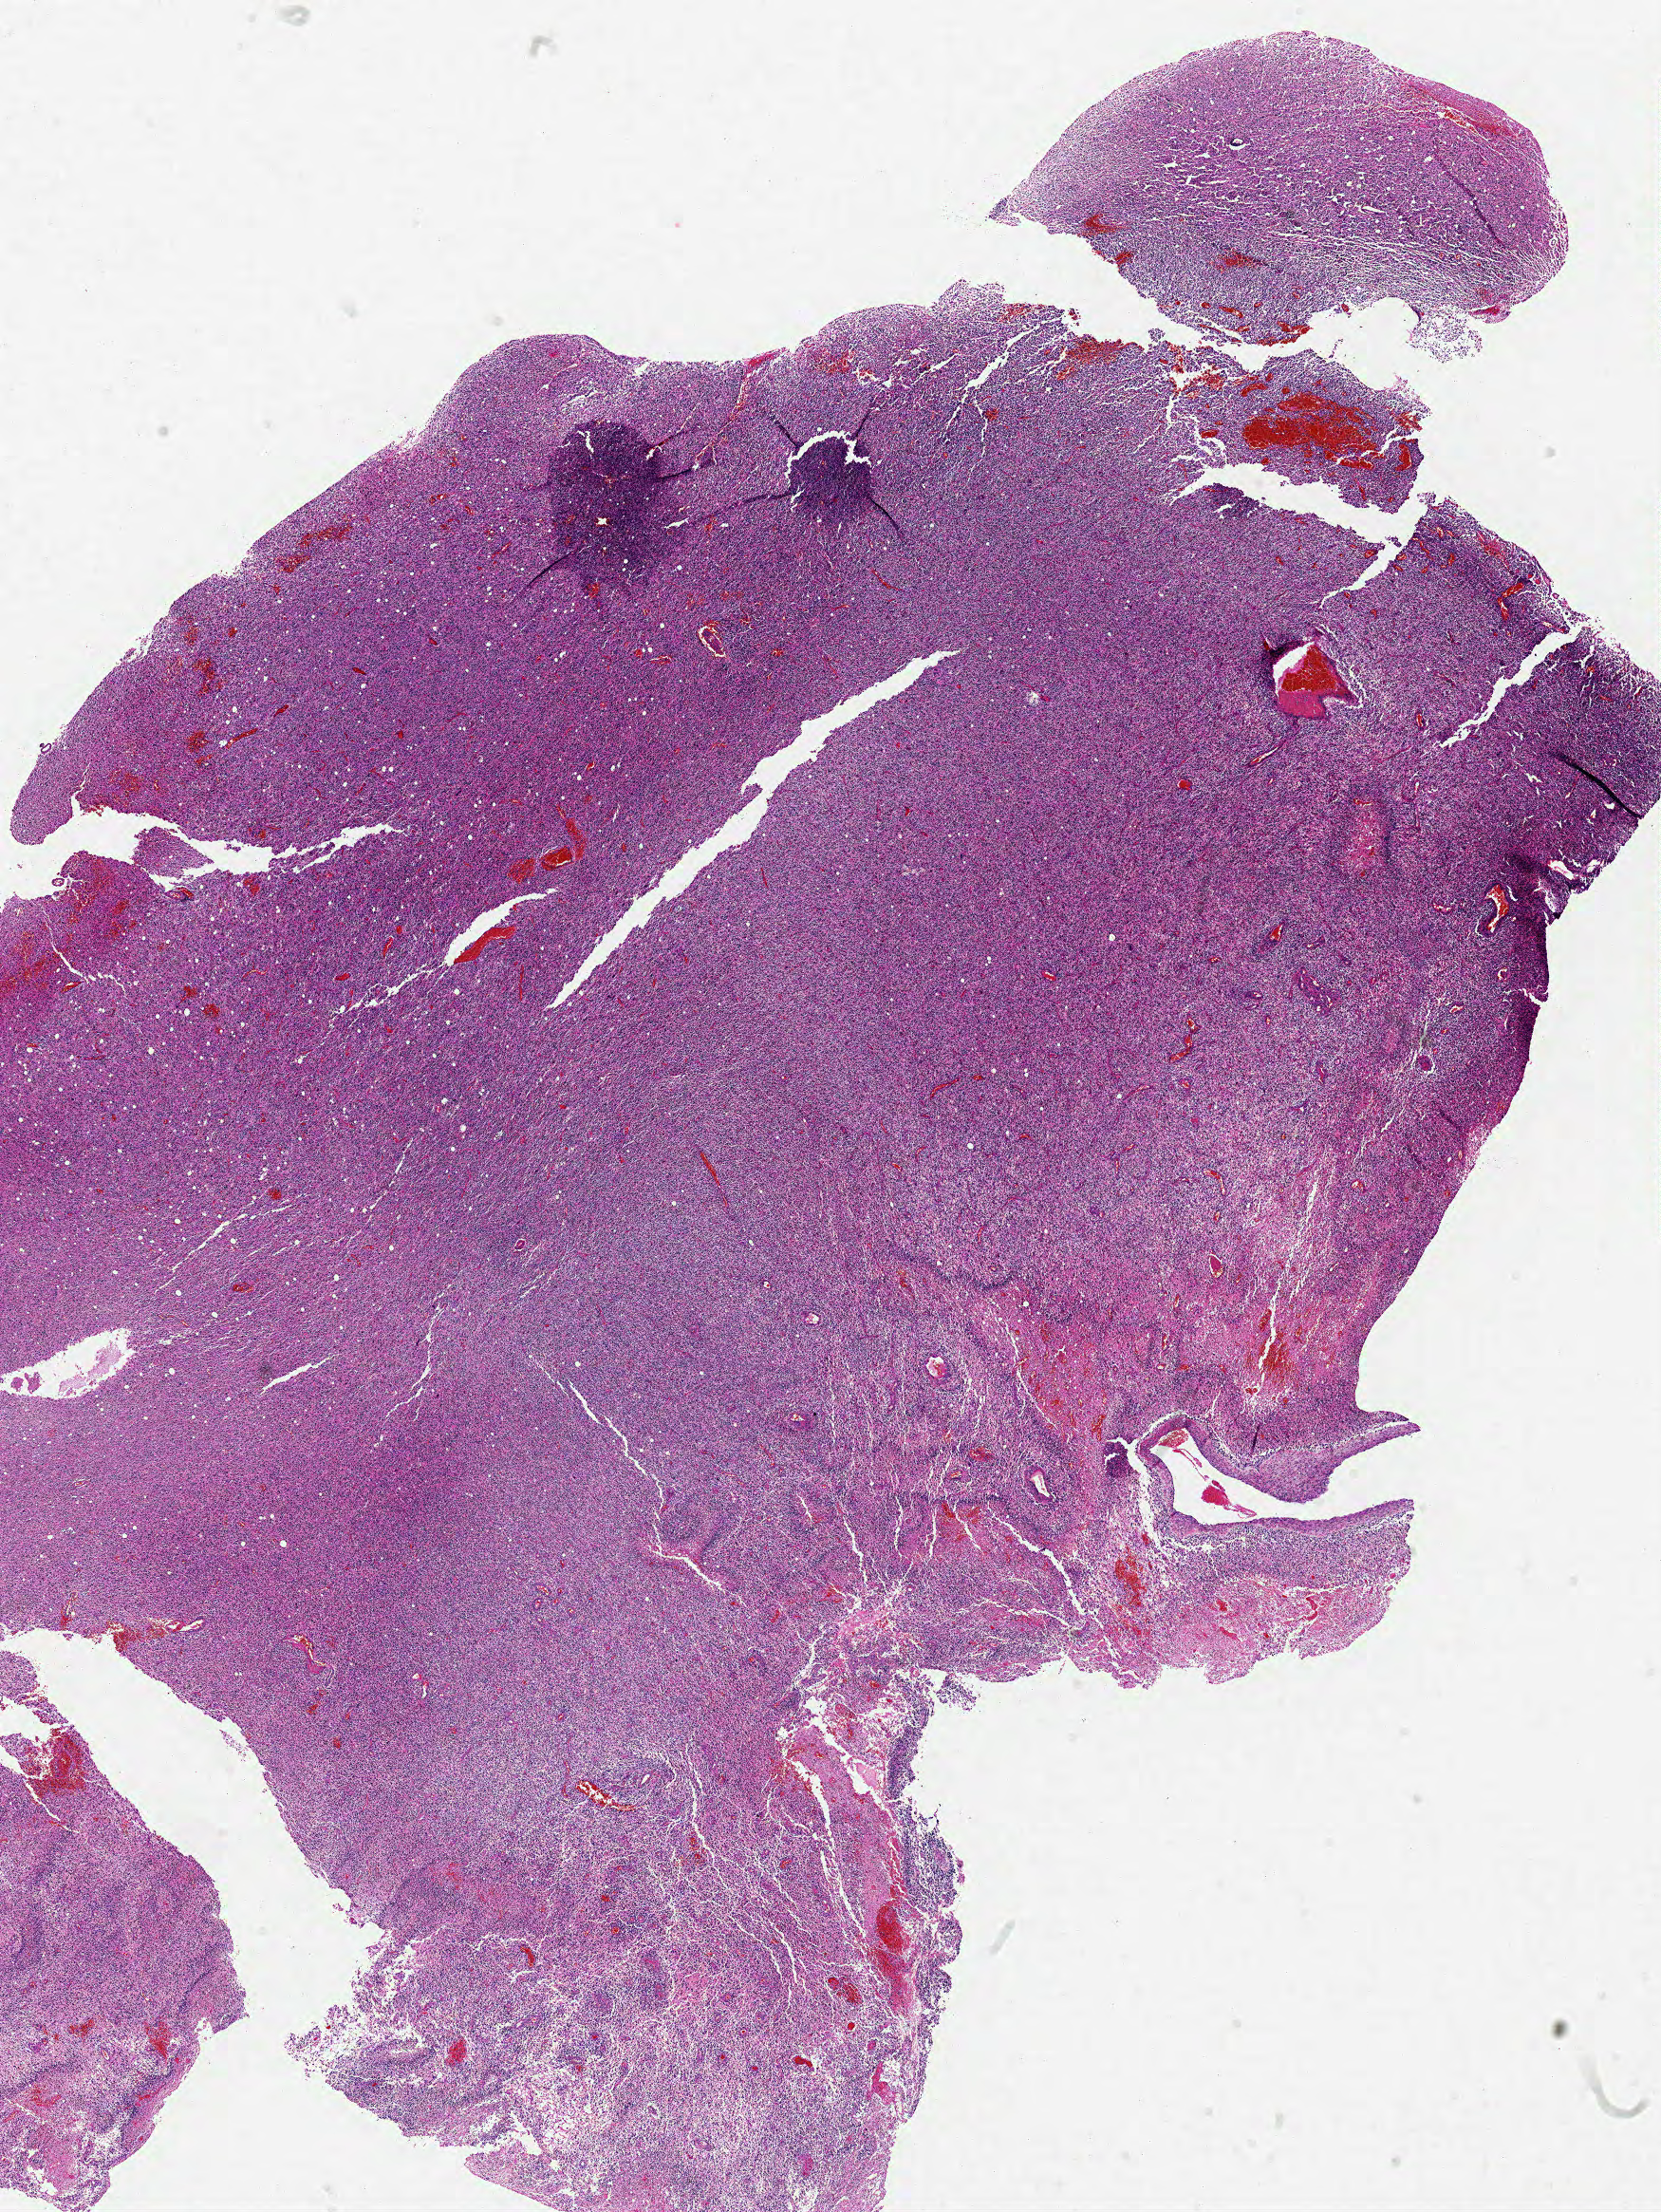
Whole-slide histology image, Hematoxylin and eosin (H&E) stained, a low-resolution overview of the entire scanned area, about 14.0 x 18.6 mm (slide scanned at 20x); formalin-fixed paraffin-embedded (FFPE) diagnostic section; brain, primary tumour sample. Female patient; age at initial diagnosis 51 years.
Diagnosis: Glioblastoma.